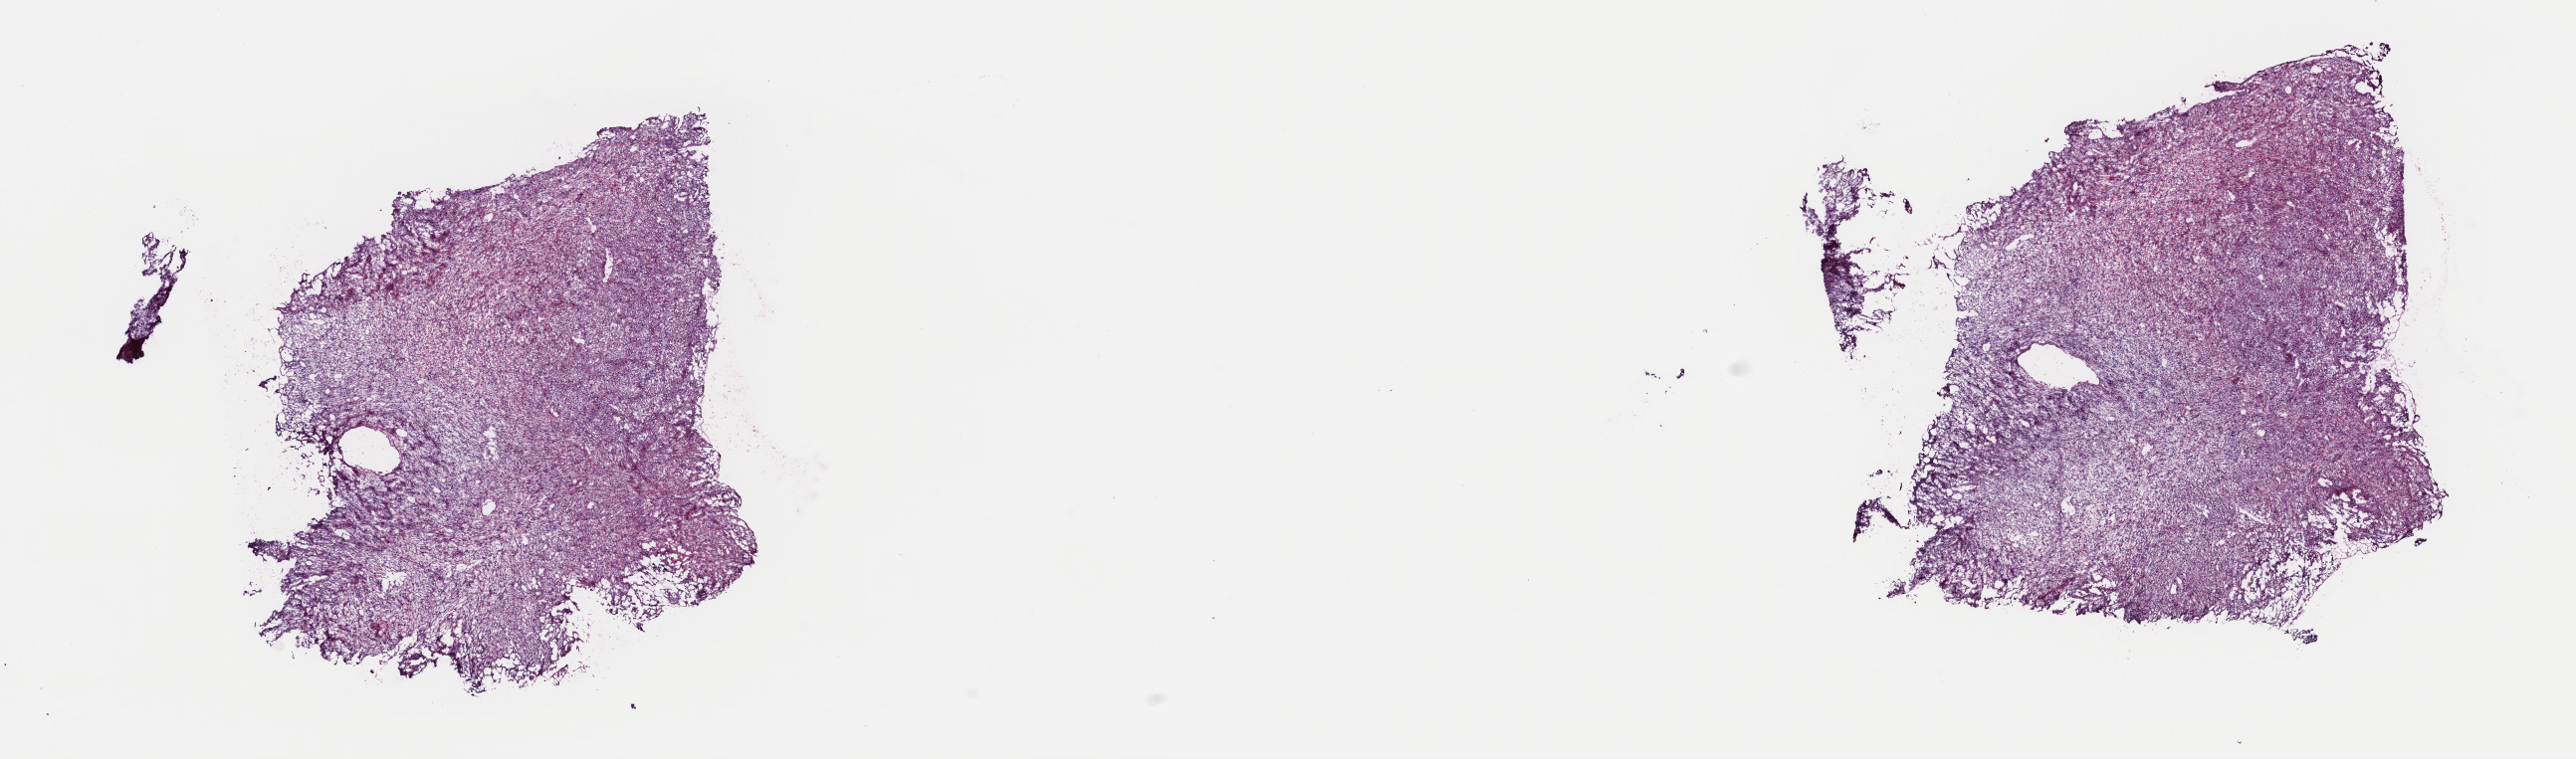
Digitized H&E tissue section (whole slide) — shown as a low-resolution overview of the whole scanned area (about 20.4 x 6.0 mm, acquisition: 40x scan), frozen section from the top of the tissue portion, peripheral nerves and autonomic nervous system, primary tumour sample. Male patient; age at initial diagnosis 50 years. Pathologist review of this section (percent, as recorded): tumour cells 100%, tumour nuclei 80%, normal cells 0%, stromal cells 0%, necrosis 0%. Infiltration values recorded for this section: lymphocyte infiltration 1%, monocyte infiltration 0%, neutrophil infiltration 0%.
• histologic diagnosis: Malignant peripheral nerve sheath tumor (peripheral nerves and autonomic nervous system of upper limb and shoulder)